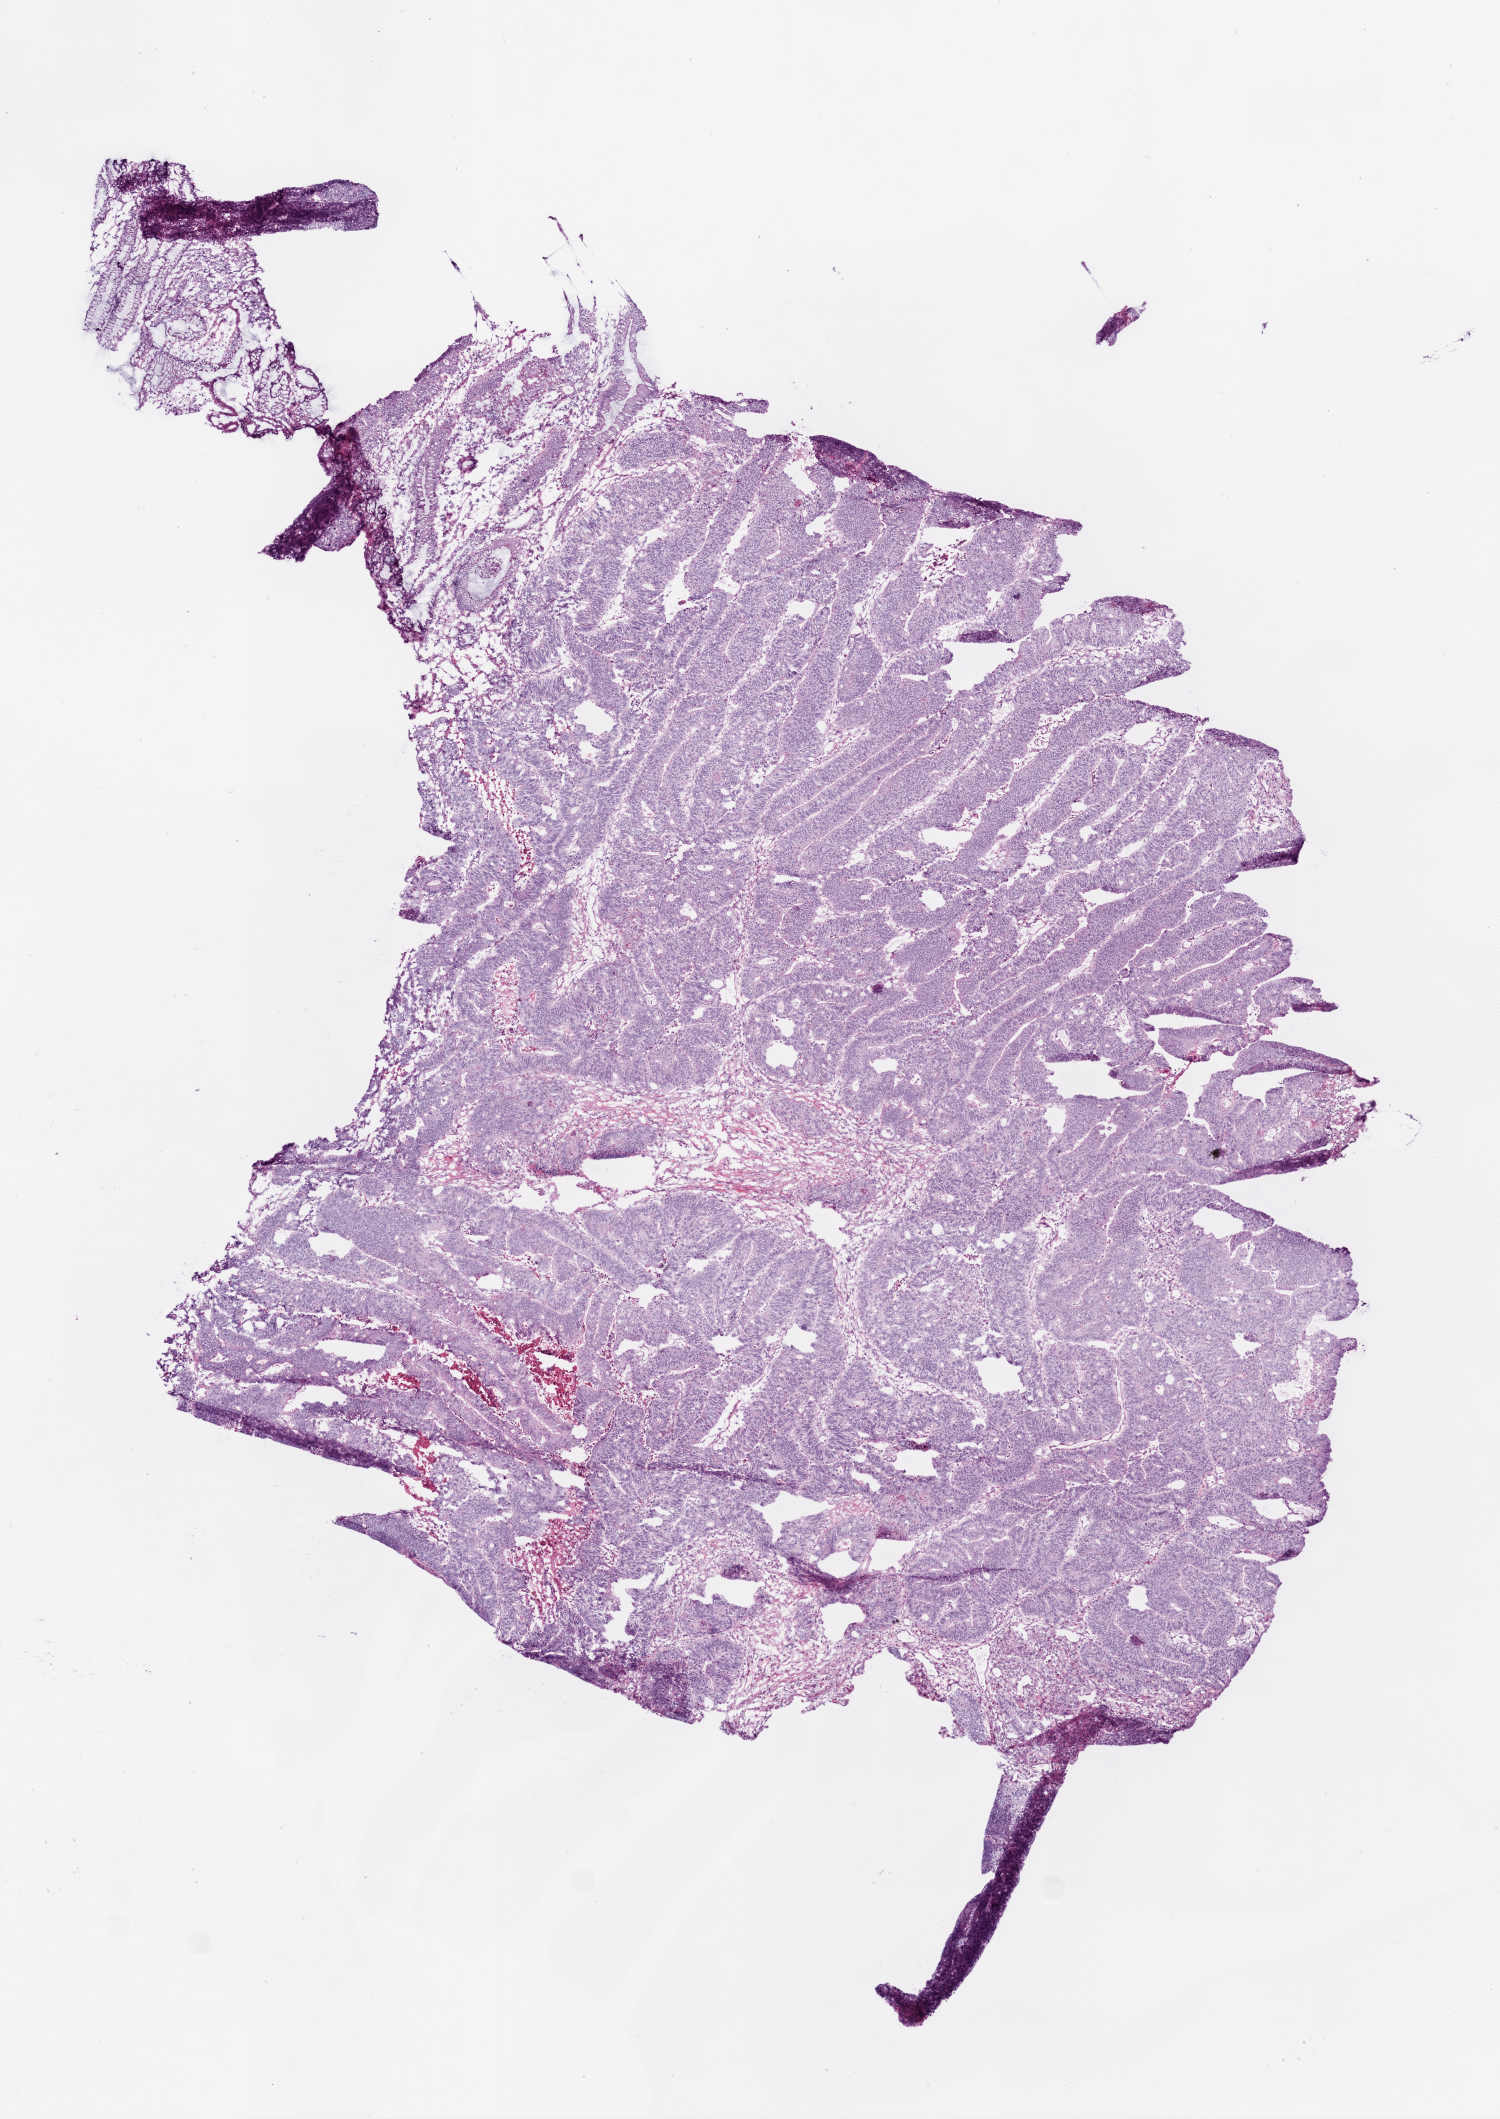
Digitized Hematoxylin and eosin (H&E) stained tissue section (whole slide) — a low-resolution overview of the entire scanned area, about 6.0 x 8.5 mm, frozen section from the top of the tissue portion, sample: primary tumour, colon. Male patient; age at initial diagnosis 84 years. Slide review estimates, as recorded: tumour cells 90%, tumour nuclei 90%, normal cells 8%, stromal cells 0%, necrosis 2%. Inflammatory infiltration, as recorded: lymphocyte infiltration 5%, neutrophil infiltration 1%.
* AJCC pathologic stage: IIA (6th edition)
* pathologic diagnosis: Adenocarcinoma, NOS
* lymph nodes positive (case pathology): 0 of 22 examined